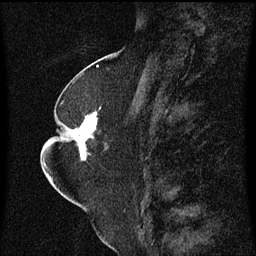
Breast MRI (dynamic contrast-enhanced), one sagittal slice. Position 30 of 60 along the scan axis. Dynamic contrast-enhanced series, image 2 of 3 at this slice position (ordered by acquisition). 1.5 T. TE 4.2 ms, TR 8.4 ms. 2 mm slice thickness. 256 × 256 image matrix, field of view 200 × 200 mm. Patient: female, 52 years. Case-level facts recorded for this patient, not image findings: setting: breast cancer imaged before/during neoadjuvant chemotherapy; receptor status: HR-positive, HER2-negative.
Annotated regions visible in this slice (semi-automatically segmented with operator editing):
- analysis volume of interest (the breast-tissue region the enhancement analysis was run in; not a lesion): box from (x=64, y=104) to (x=110, y=161) px
- tumour enhancement mask (voxels above the 70 % enhancement threshold inside the analysis volume of interest): (x=75, y=112)–(x=97, y=161)